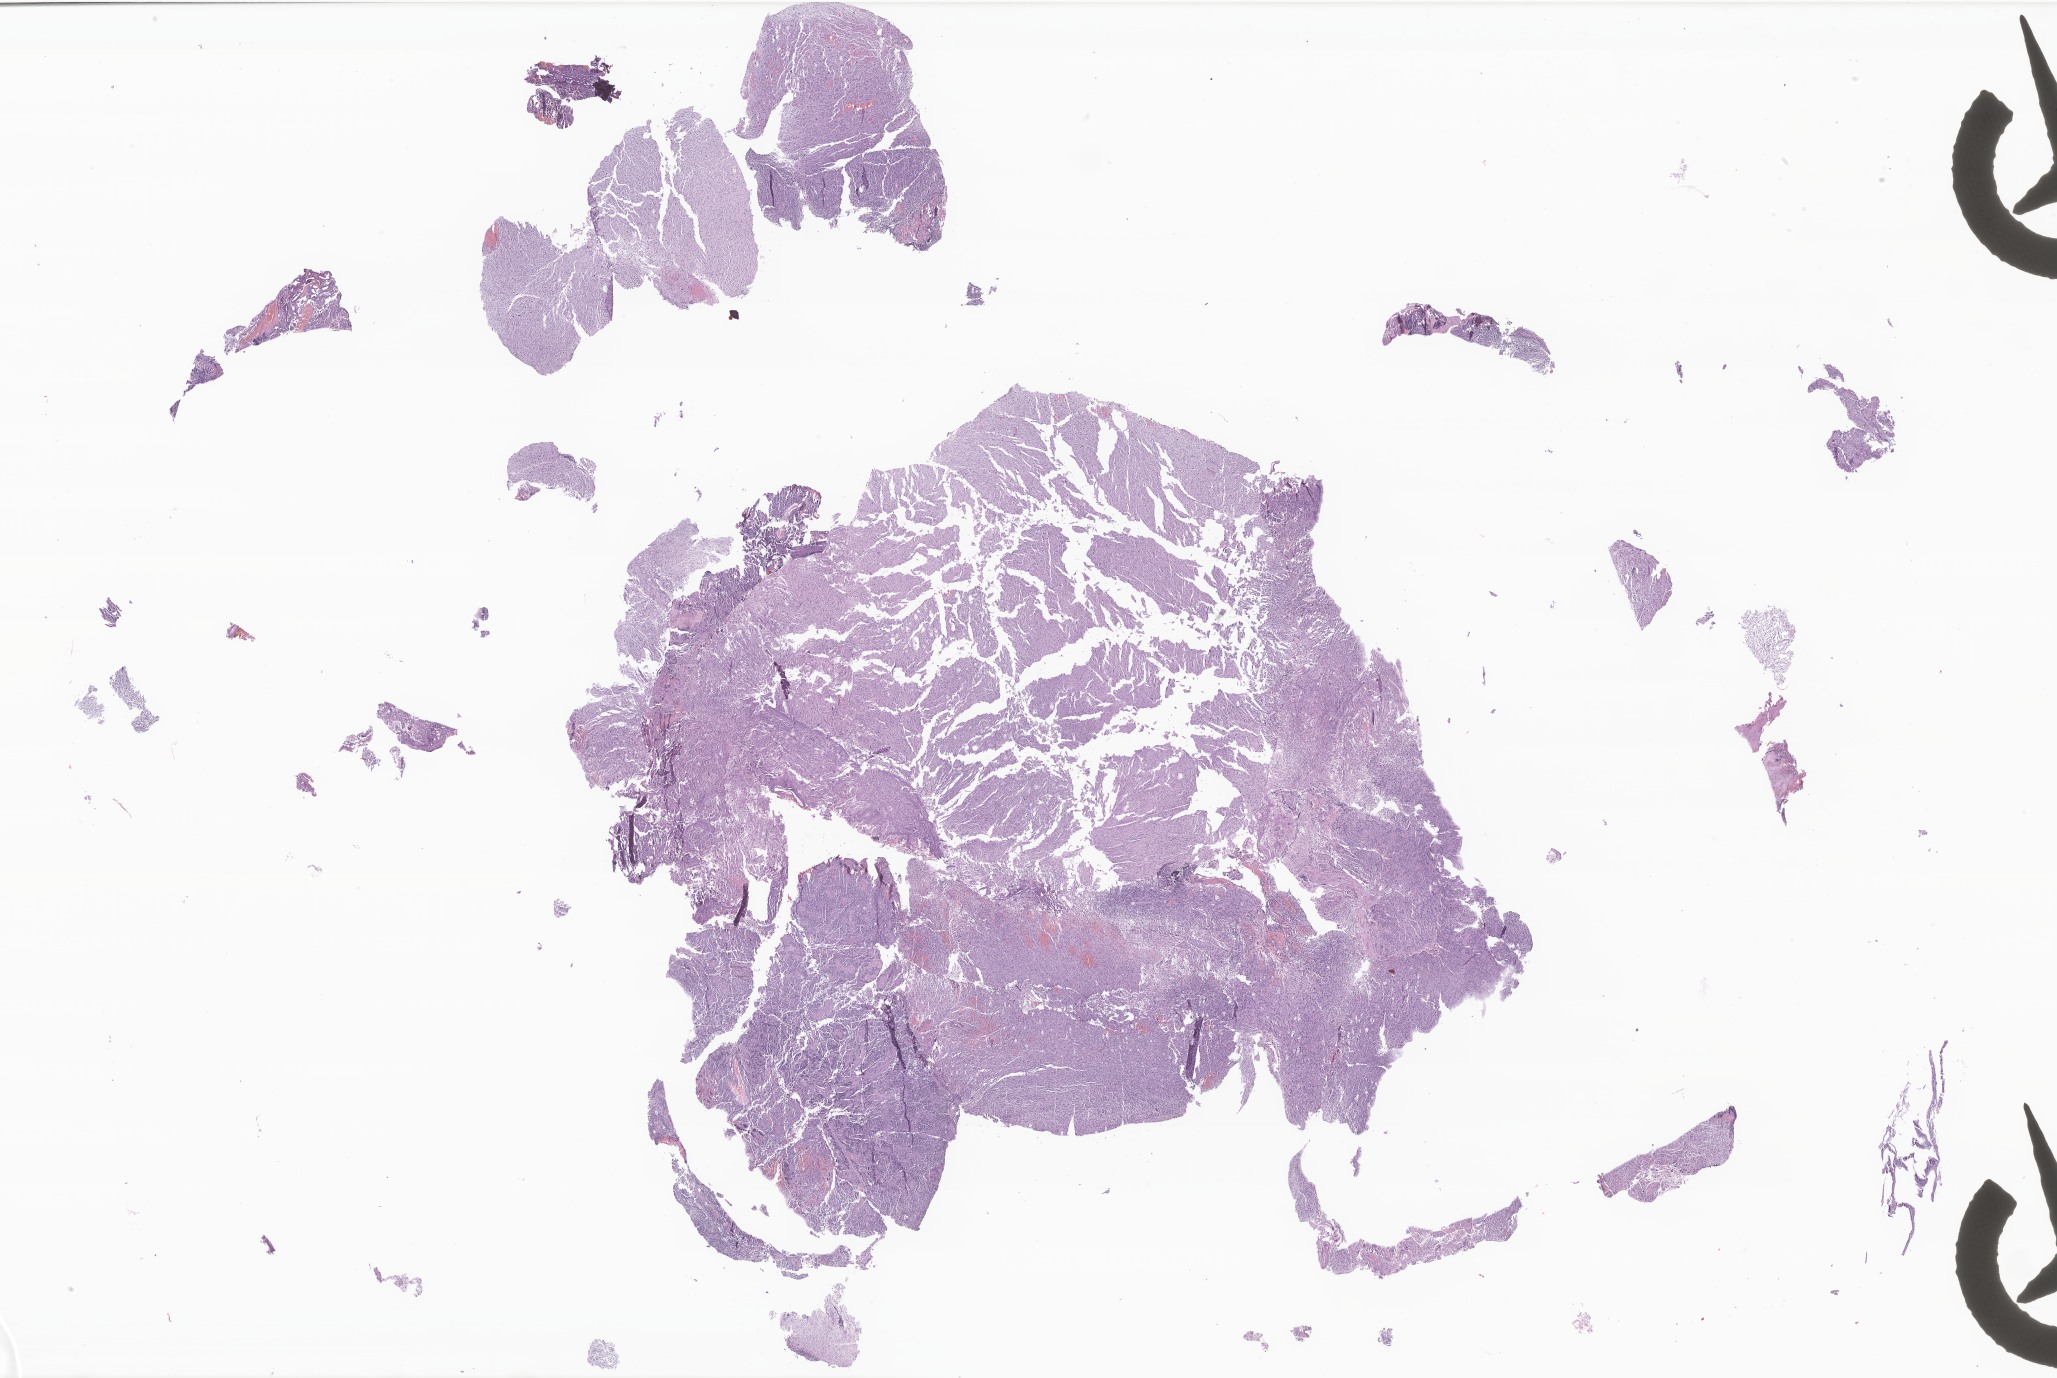
Whole-slide image, H&E stain of tumor tissue from the parietal lobe — low-resolution overview of the scanned area, about 34.7 x 23.2 mm; FFPE section. Patient: female, age 123 months (10 years 3 months).
Diagnosis: Glioma, malignant.